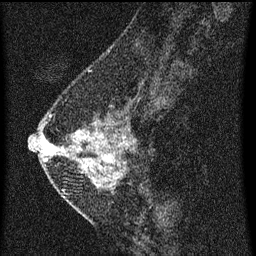
Breast MRI (dynamic contrast-enhanced), one sagittal slice; position 23 of 60 along the scan axis; dynamic contrast-enhanced series, image 2 of 3 at this slice position (ordered by acquisition); 1.5 T; TE 4.2 ms, TR 8 ms; 2 mm slice thickness; 256 × 256 image matrix. Patient: female, 47 years.
Outlined on this slice (semi-automatically segmented with operator editing):
- analysis volume of interest (the breast-tissue region the enhancement analysis was run in; not a lesion): box from (x=42, y=92) to (x=140, y=199) px
- tumour enhancement mask (voxels above the 70 % enhancement threshold inside the analysis volume of interest): (x=45, y=138)–(x=127, y=187)